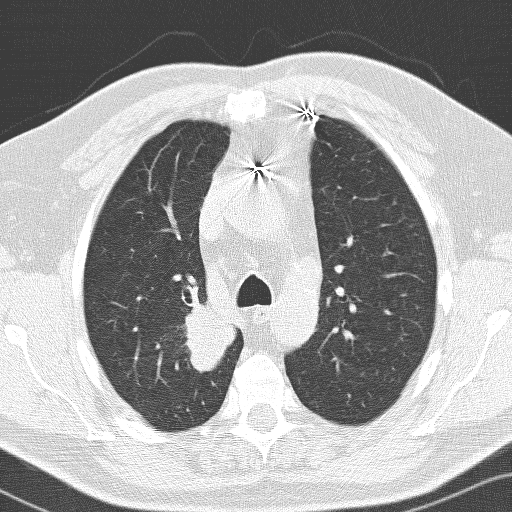
Low-dose screening chest CT, one axial slice; slice 105 of 141 in the series (ordered by position); lung window (W 1500 / L -600 HU); 3.2 mm slice thickness; 512 × 512 image matrix, field of view 326 × 326 mm.
Structures marked on this image (expert manual segmentation):
- lesion 1 (tumor, upper lobe of right lung): bounding box [x1, y1, x2, y2] px = [185, 297, 236, 373]